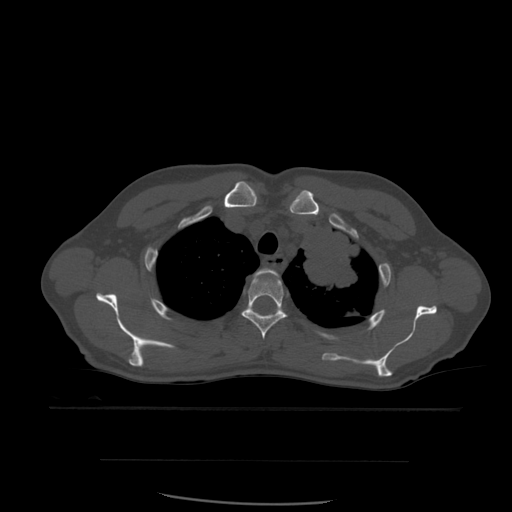
CT including the spine, one axial slice; position 442 of 574 along the scan axis; bone window (W 1800 / L 400 HU); 1.25 mm slice thickness; 512 × 512 image matrix. Patient age 48 years. From the clinical record (not read from this slice): primary cancer: lung.
Structures marked on this image (semi-automatically segmented with operator editing):
- T2 vertebra: bounding box <255,268,281,281> (left, top, right, bottom; pixels)
- T3 vertebra: <242,273,287,340>